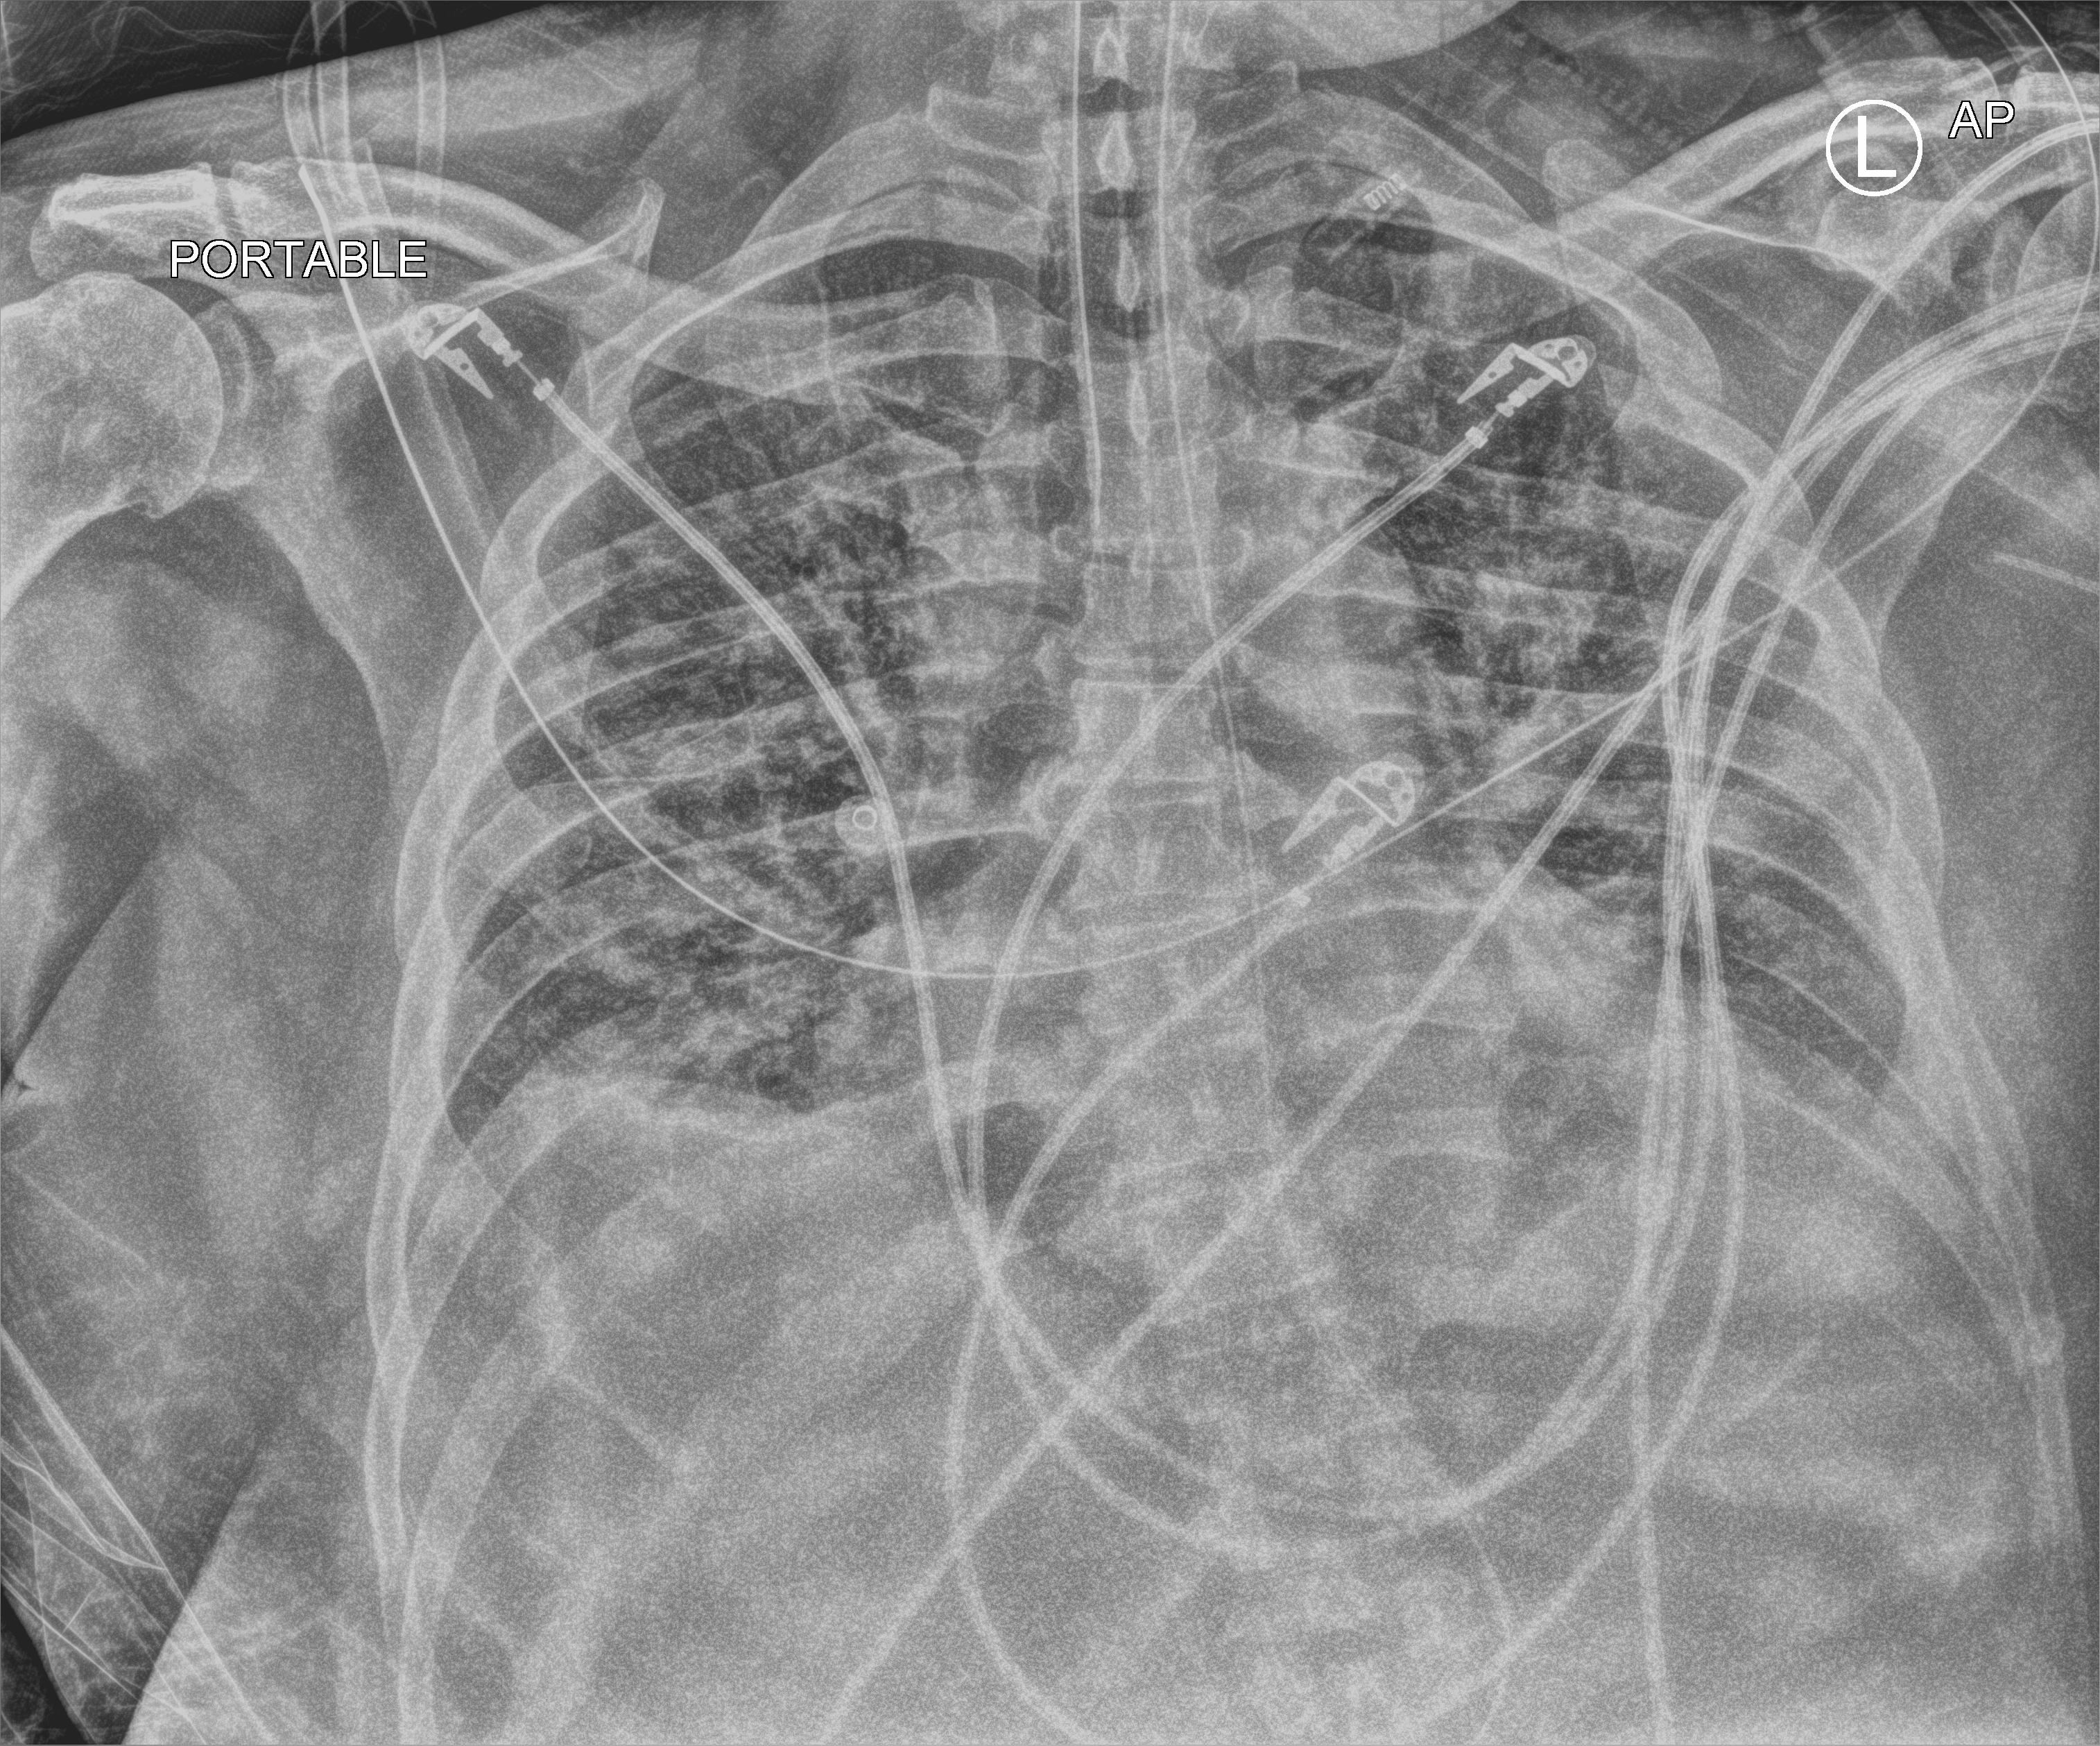
Chest X-ray (portable); anteroposterior (AP) projection. Male patient hospitalised with COVID-19, age 18–59 years.
From the hospital-stay record, not from the radiograph (when in the stay this image was taken is not recorded):
- mechanically ventilated during this hospital stay: yes
- COPD (admission record): no
- admitted to intensive care during this hospital stay: yes